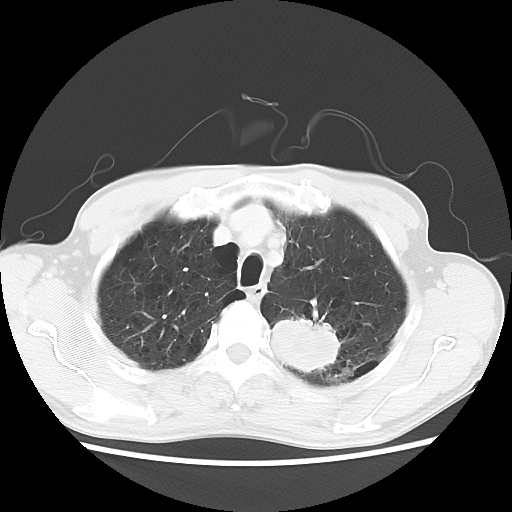
Chest CT, one axial slice. Slice 52 of 64 in the series (ordered by position). Reconstruction kernel LUNG. 120 kVp. Lung window (W 1500 / L -600 HU). 5 mm slice thickness. 512 × 512 image matrix, field of view 346 × 346 mm. Patient: male, 63 years. From the clinical record (not read from this slice): clinical TNM (as recorded): T2 N0 M0.
Annotated regions visible in this slice (bounding box drawn by a radiologist):
- lung tumour (recorded histology: adenocarcinoma): box from (x=268, y=307) to (x=349, y=389) px